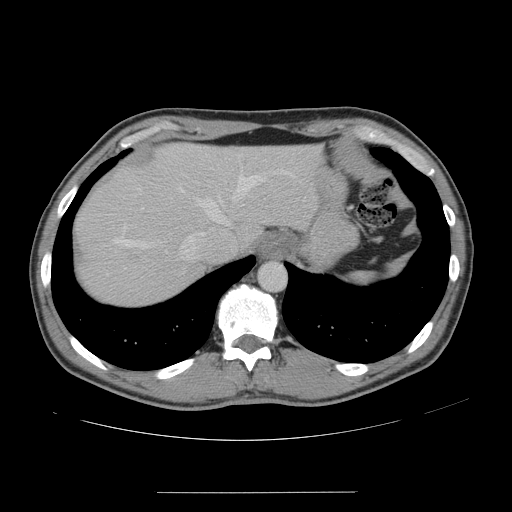
Contrast-enhanced abdominal CT, one axial slice; intravenous contrast given; soft-tissue window (W 400 / L 40 HU); 2.5 mm slice thickness; 512 × 512 image matrix, field of view 401 × 401 mm. Male patient, age 53 years. Case-level facts recorded for this patient, not image findings: diagnosis: colorectal cancer liver metastases, imaged before liver resection; multiple liver metastases: yes; largest metastasis: 2.4 cm; disease in both lobes: no.
Annotated regions visible in this slice (expert manual segmentation):
- hepatic veins: bounding box [x1, y1, x2, y2] px = [113, 170, 291, 259]
- liver: [76, 143, 319, 306]
- planned liver remnant (the part of the liver to remain after resection): [158, 143, 317, 242]